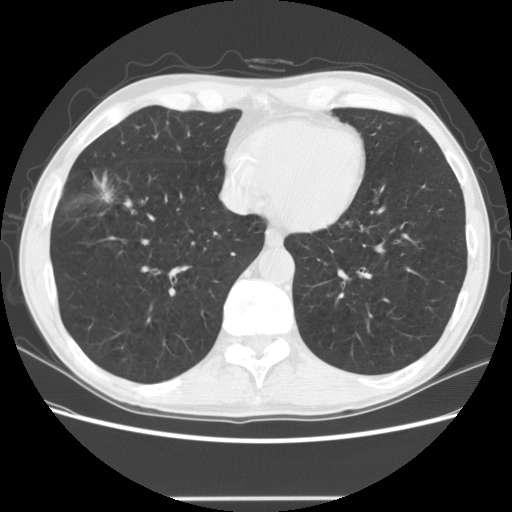
Low-dose screening chest CT, one axial slice. Slice 49 of 145 in the series (ordered by position). Lung window (W 1500 / L -600 HU). 2.5 mm slice thickness. 512 × 512 image matrix, field of view 365 × 365 mm.
Structures marked on this image (expert manual segmentation):
- lesion 1 (tumor, middle lobe of right lung): bounding box [x1, y1, x2, y2] px = [94, 173, 113, 203]